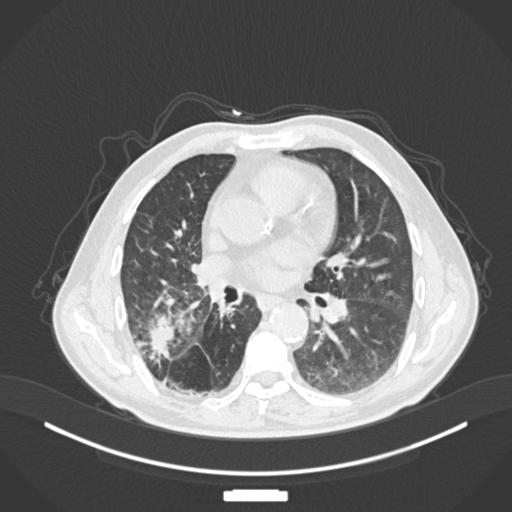
Chest CT, one axial slice; slice 82 of 201 in the series (ordered by position); reconstruction kernel B30f; lung window (W 1500 / L -600 HU); 1 mm slice thickness; 512 × 512 image matrix, field of view 400 × 400 mm. Male patient, age 72 years. Case-level facts recorded for this patient, not image findings: clinical TNM (as recorded): T3 N2 M0.
Structures marked on this image (bounding box drawn by a radiologist):
- lung tumour (recorded histology: adenocarcinoma): bounding box (x1, y1, x2, y2) in pixels: (143, 316, 175, 364)